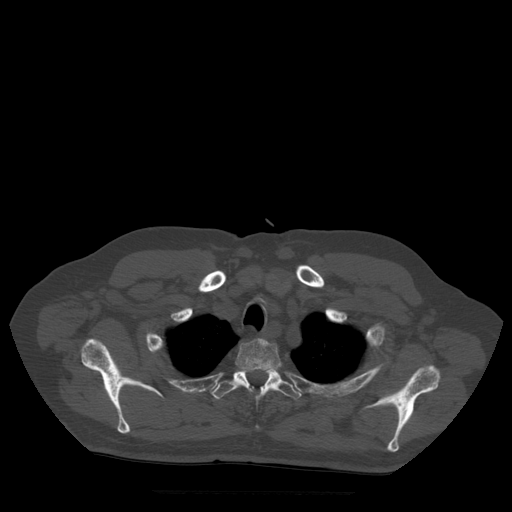
CT including the spine, one axial slice. Position 416 of 522 along the scan axis. Bone window (W 1800 / L 400 HU). 512 × 512 image matrix, field of view 420 × 420 mm. Patient age 72 years. Case-level facts recorded for this patient, not image findings: primary cancer: prostate.
Structures marked on this image (semi-automatically segmented with operator editing):
- T2 vertebra: bounding box [x1, y1, x2, y2] px = [236, 338, 284, 383]
- T3 vertebra: [211, 369, 302, 430]